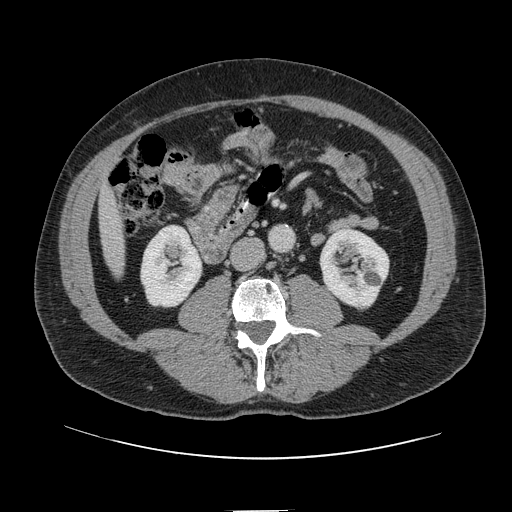
Contrast-enhanced abdominal CT, one axial slice; 120 kVp; soft-tissue window (W 400 / L 40 HU); 2.5 mm slice thickness; 512 × 512 image matrix. Male patient, age 66 years. From the clinical record (not read from this slice): diagnosis: colorectal cancer liver metastases, imaged before liver resection; multiple liver metastases: no; largest metastasis: 3.5 cm; disease in both lobes: no.
Structures marked on this image (manually delineated by an expert):
- liver: bounding box (x1, y1, x2, y2) in pixels: (101, 191, 124, 275)
- planned liver remnant (the part of the liver to remain after resection): (101, 190, 120, 242)